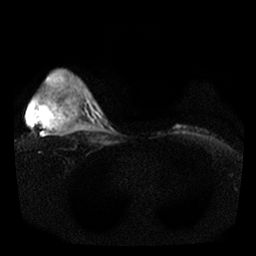
Breast MRI, one axial slice. Slice 24 of 25 in the series (ordered by position). Diffusion-weighted series; image 2 of 4 stored at this slice position (different b-values; order by instance number). 1.5 T. 4 mm slice thickness. 256 × 256 image matrix, field of view 350 × 350 mm. Female patient.
Outlined on this slice (expert manual segmentation):
- tumour on diffusion-weighted imaging: box from (x=70, y=88) to (x=84, y=121) px